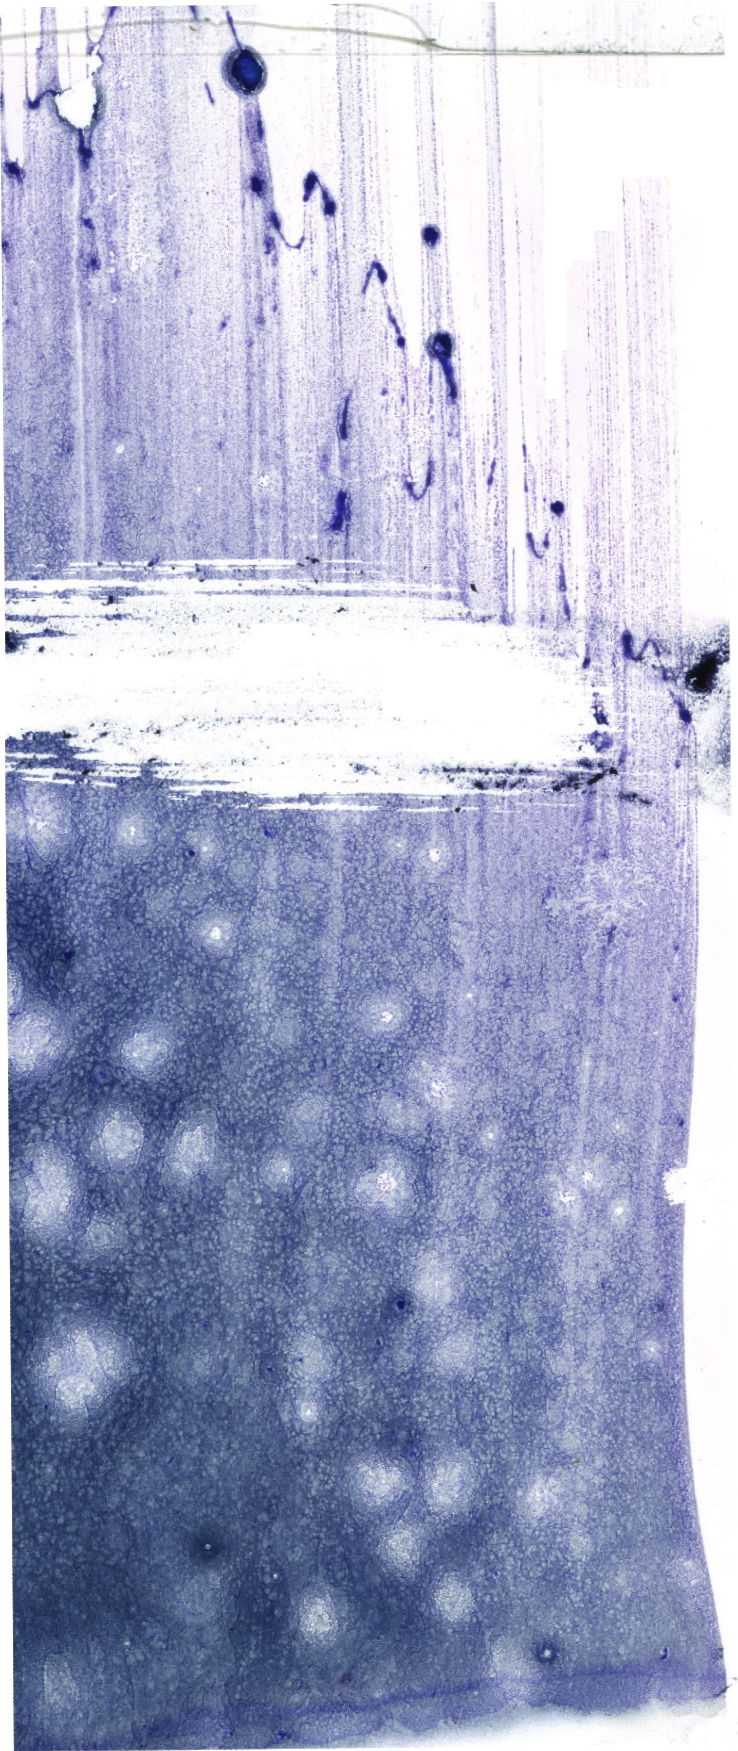
May-Grünwald–Giemsa-stained marrow aspirate smear (whole slide) — a low-resolution overview of the entire scanned area, about 20.9 x 49.6 mm. Male patient.
• diagnosis: Acute Monocytic Leukemia